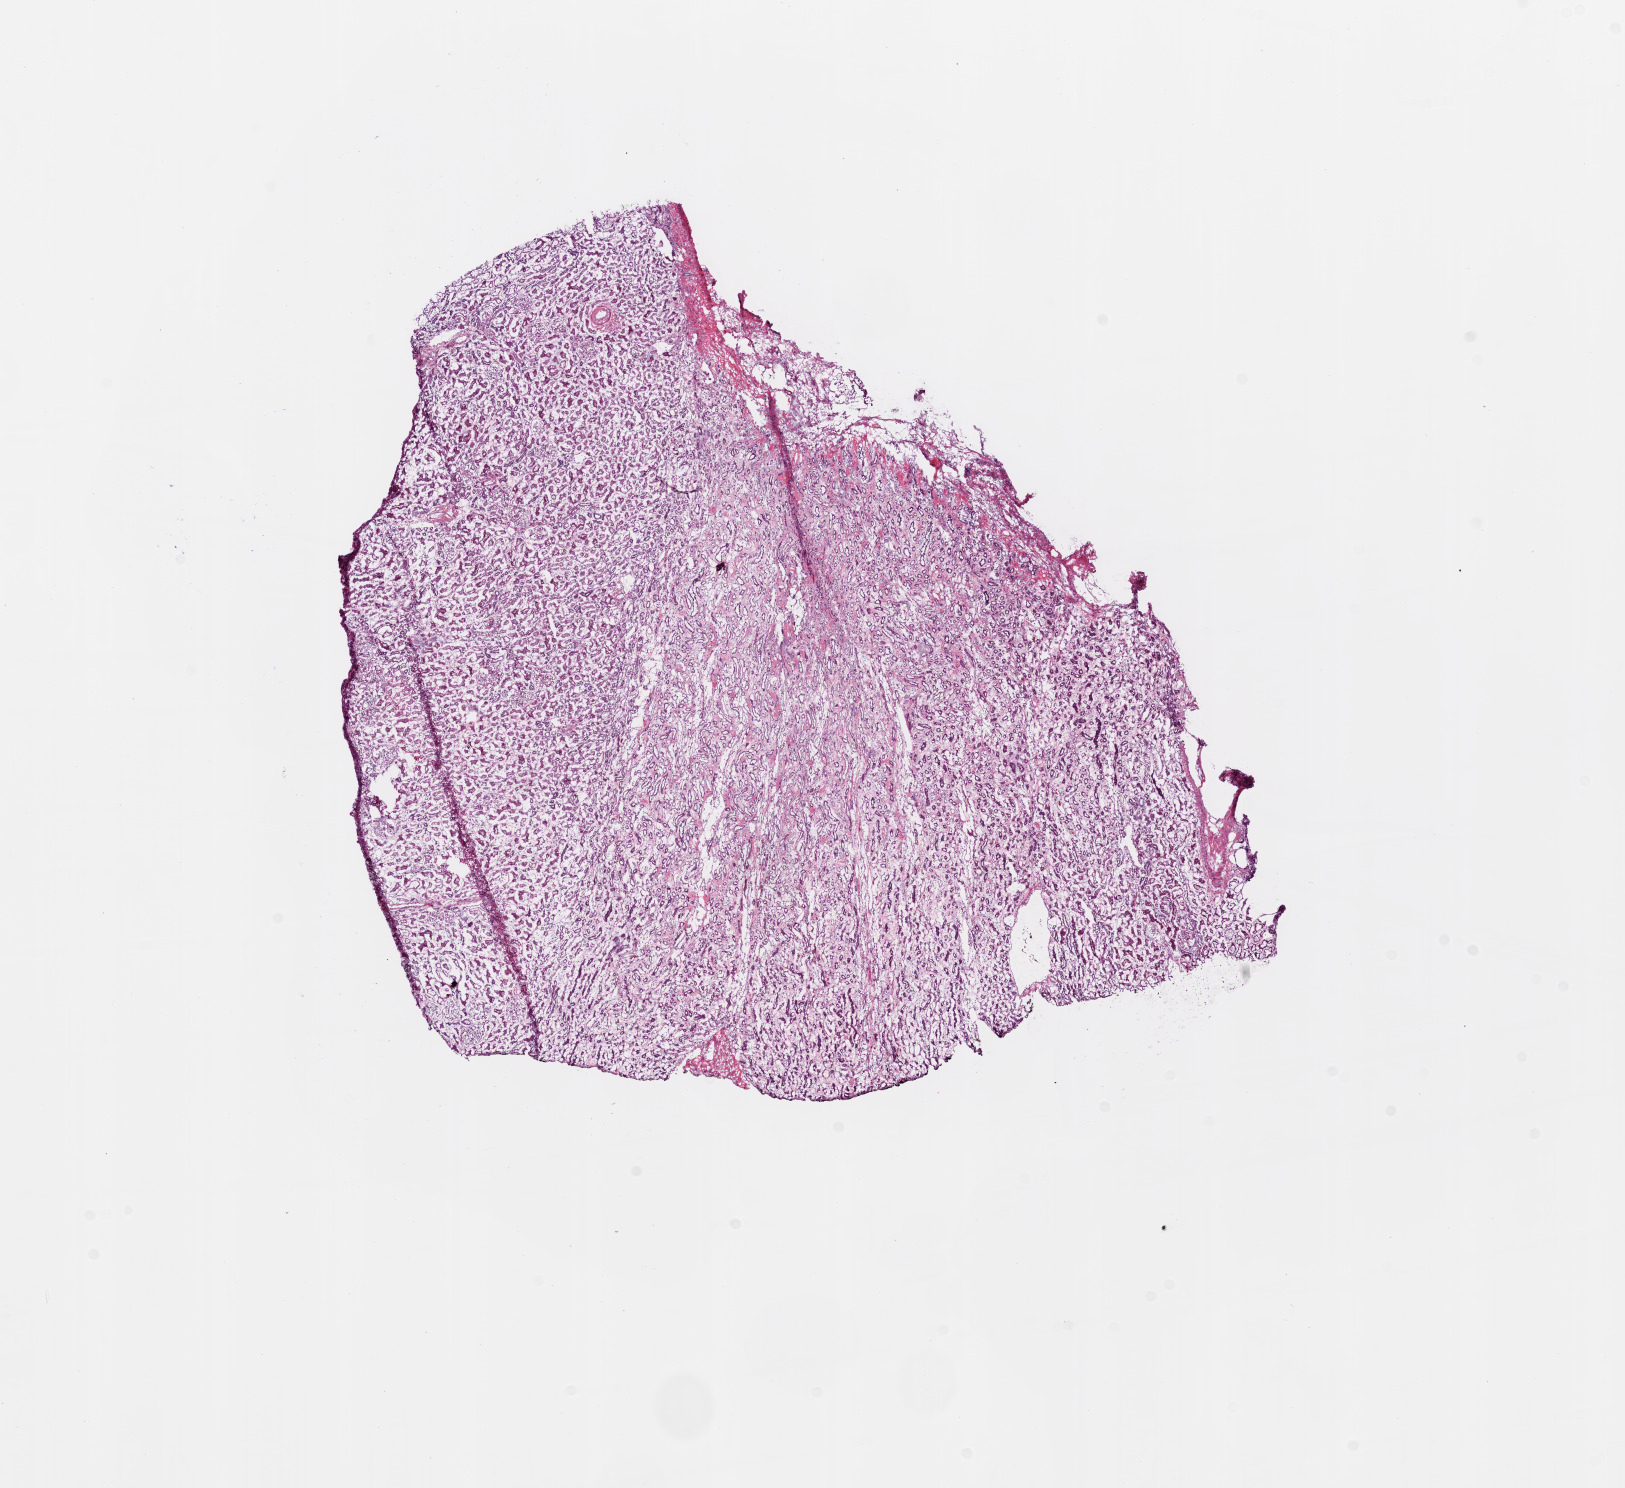
Digitized Hematoxylin and eosin (H&E) stained tissue section (whole slide), low-resolution overview of the scanned area, about 13.0 x 11.9 mm (acquisition: 20x scan). Frozen section from the top of the tissue portion. Kidney, solid tissue normal (non-tumour tissue) sample. Female, age 54 years at initial diagnosis.
This section: solid tissue normal sample (biorepository sample class). Patient diagnosis: Clear cell adenocarcinoma, NOS.